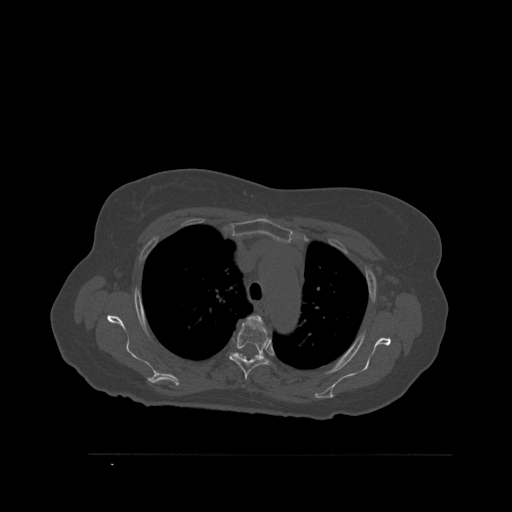
CT including the spine, one axial slice; slice 408 of 527 in the series (ordered by position); bone window (W 1800 / L 400 HU); 1.5 mm slice thickness; 512 × 512 image matrix. Patient: female, 73 years. Case-level facts recorded for this patient, not image findings: primary cancer: breast; vertebrae with lytic lesions (as recorded): L2.
Structures marked on this image (semi-automatically segmented with operator editing):
- T3 vertebra: bounding box <249,315,262,322> (left, top, right, bottom; pixels)
- T4 vertebra: <228,319,269,380>